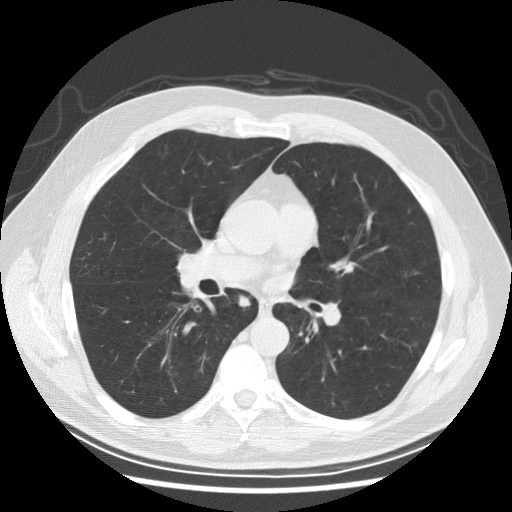
Low-dose screening chest CT, axial slice, second screening round (one year after baseline), lung window (W 1500 / L -600 HU), 2.5 mm slice thickness, slice 115 of 246 in the series. Male, age 61 years at enrolment. Former smoker at enrolment.
Expert reader's lesion annotation, bounding box [x1, y1, x2, y2] px = [225, 285, 257, 317]. No non-calcified nodule or mass ≥4 mm was recorded by the screening reader at this exam. Official screen result: negative screen, minor abnormalities not suspicious for lung cancer. Lung cancer was diagnosed 382 days after this screen: squamous cell carcinoma, keratinizing, NOS, right lower lobe, stage IIIB (AJCC 6th edition), 40 mm at pathology.